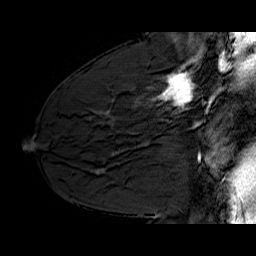
Breast MRI (dynamic contrast-enhanced), one sagittal slice. Dynamic contrast-enhanced series, time point 2 of 6 at this slice position (early post-contrast). 1.5 T. TE 6.4 ms, TR 32.9 ms. 256 × 256 image matrix, field of view 200 × 200 mm. Female patient. From the clinical record (not read from this slice): setting: breast cancer imaged before/during neoadjuvant chemotherapy; receptor status: HER2-positive.
Outlined on this slice (semi-automatically segmented with operator editing):
- analysis volume of interest (the breast-tissue region the enhancement analysis was run in; not a lesion): bounding box (x1, y1, x2, y2) in pixels: (130, 62, 210, 128)
- tumour enhancement mask (voxels above the 100 % enhancement threshold inside the analysis volume of interest): (152, 62, 193, 106)